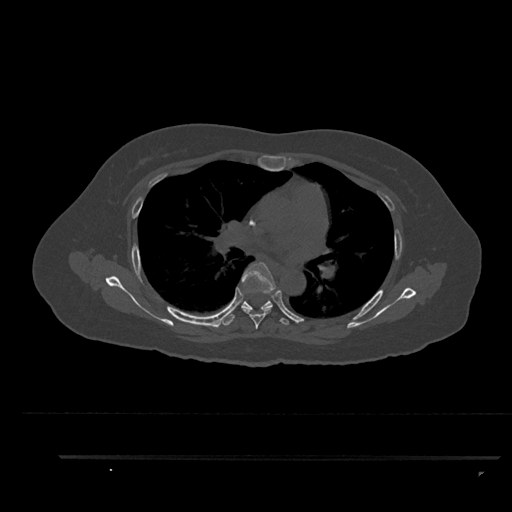
CT including the spine, one axial slice; slice 582 of 797 in the series (ordered by position); reconstruction kernel Br40s/3; 120 kVp; bone window (W 1800 / L 400 HU); 0.5 mm slice thickness; 512 × 512 image matrix, field of view 408 × 408 mm. Patient: female, 44 years. Case-level facts recorded for this patient, not image findings: primary cancer: renal; vertebrae with lytic lesions (as recorded): L1.
Outlined on this slice (semi-automatic segmentation, software-assisted and operator-edited):
- T5 vertebra: bounding box [x1, y1, x2, y2] px = [241, 262, 276, 329]
- T6 vertebra: [223, 300, 289, 326]